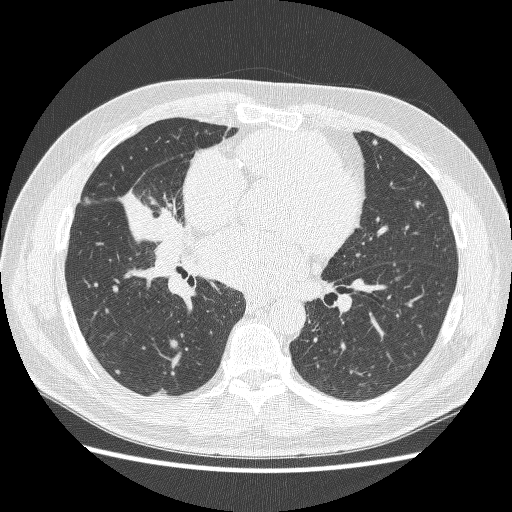
Chest CT (low-dose screening protocol), one axial image; first (baseline) screen; lung window (W 1500 / L -600 HU); lung (sharp) reconstruction kernel (BONE); 120 kVp; slice 130 of 251 in the series. Male participant, aged 59 years at enrolment. Former smoker at enrolment.
Lesion marked by an expert reader, bounding box (x1, y1, x2, y2) in pixels: (115, 172, 196, 253). Screening reader's record for this exam: no non-calcified nodule ≥4 mm recorded.